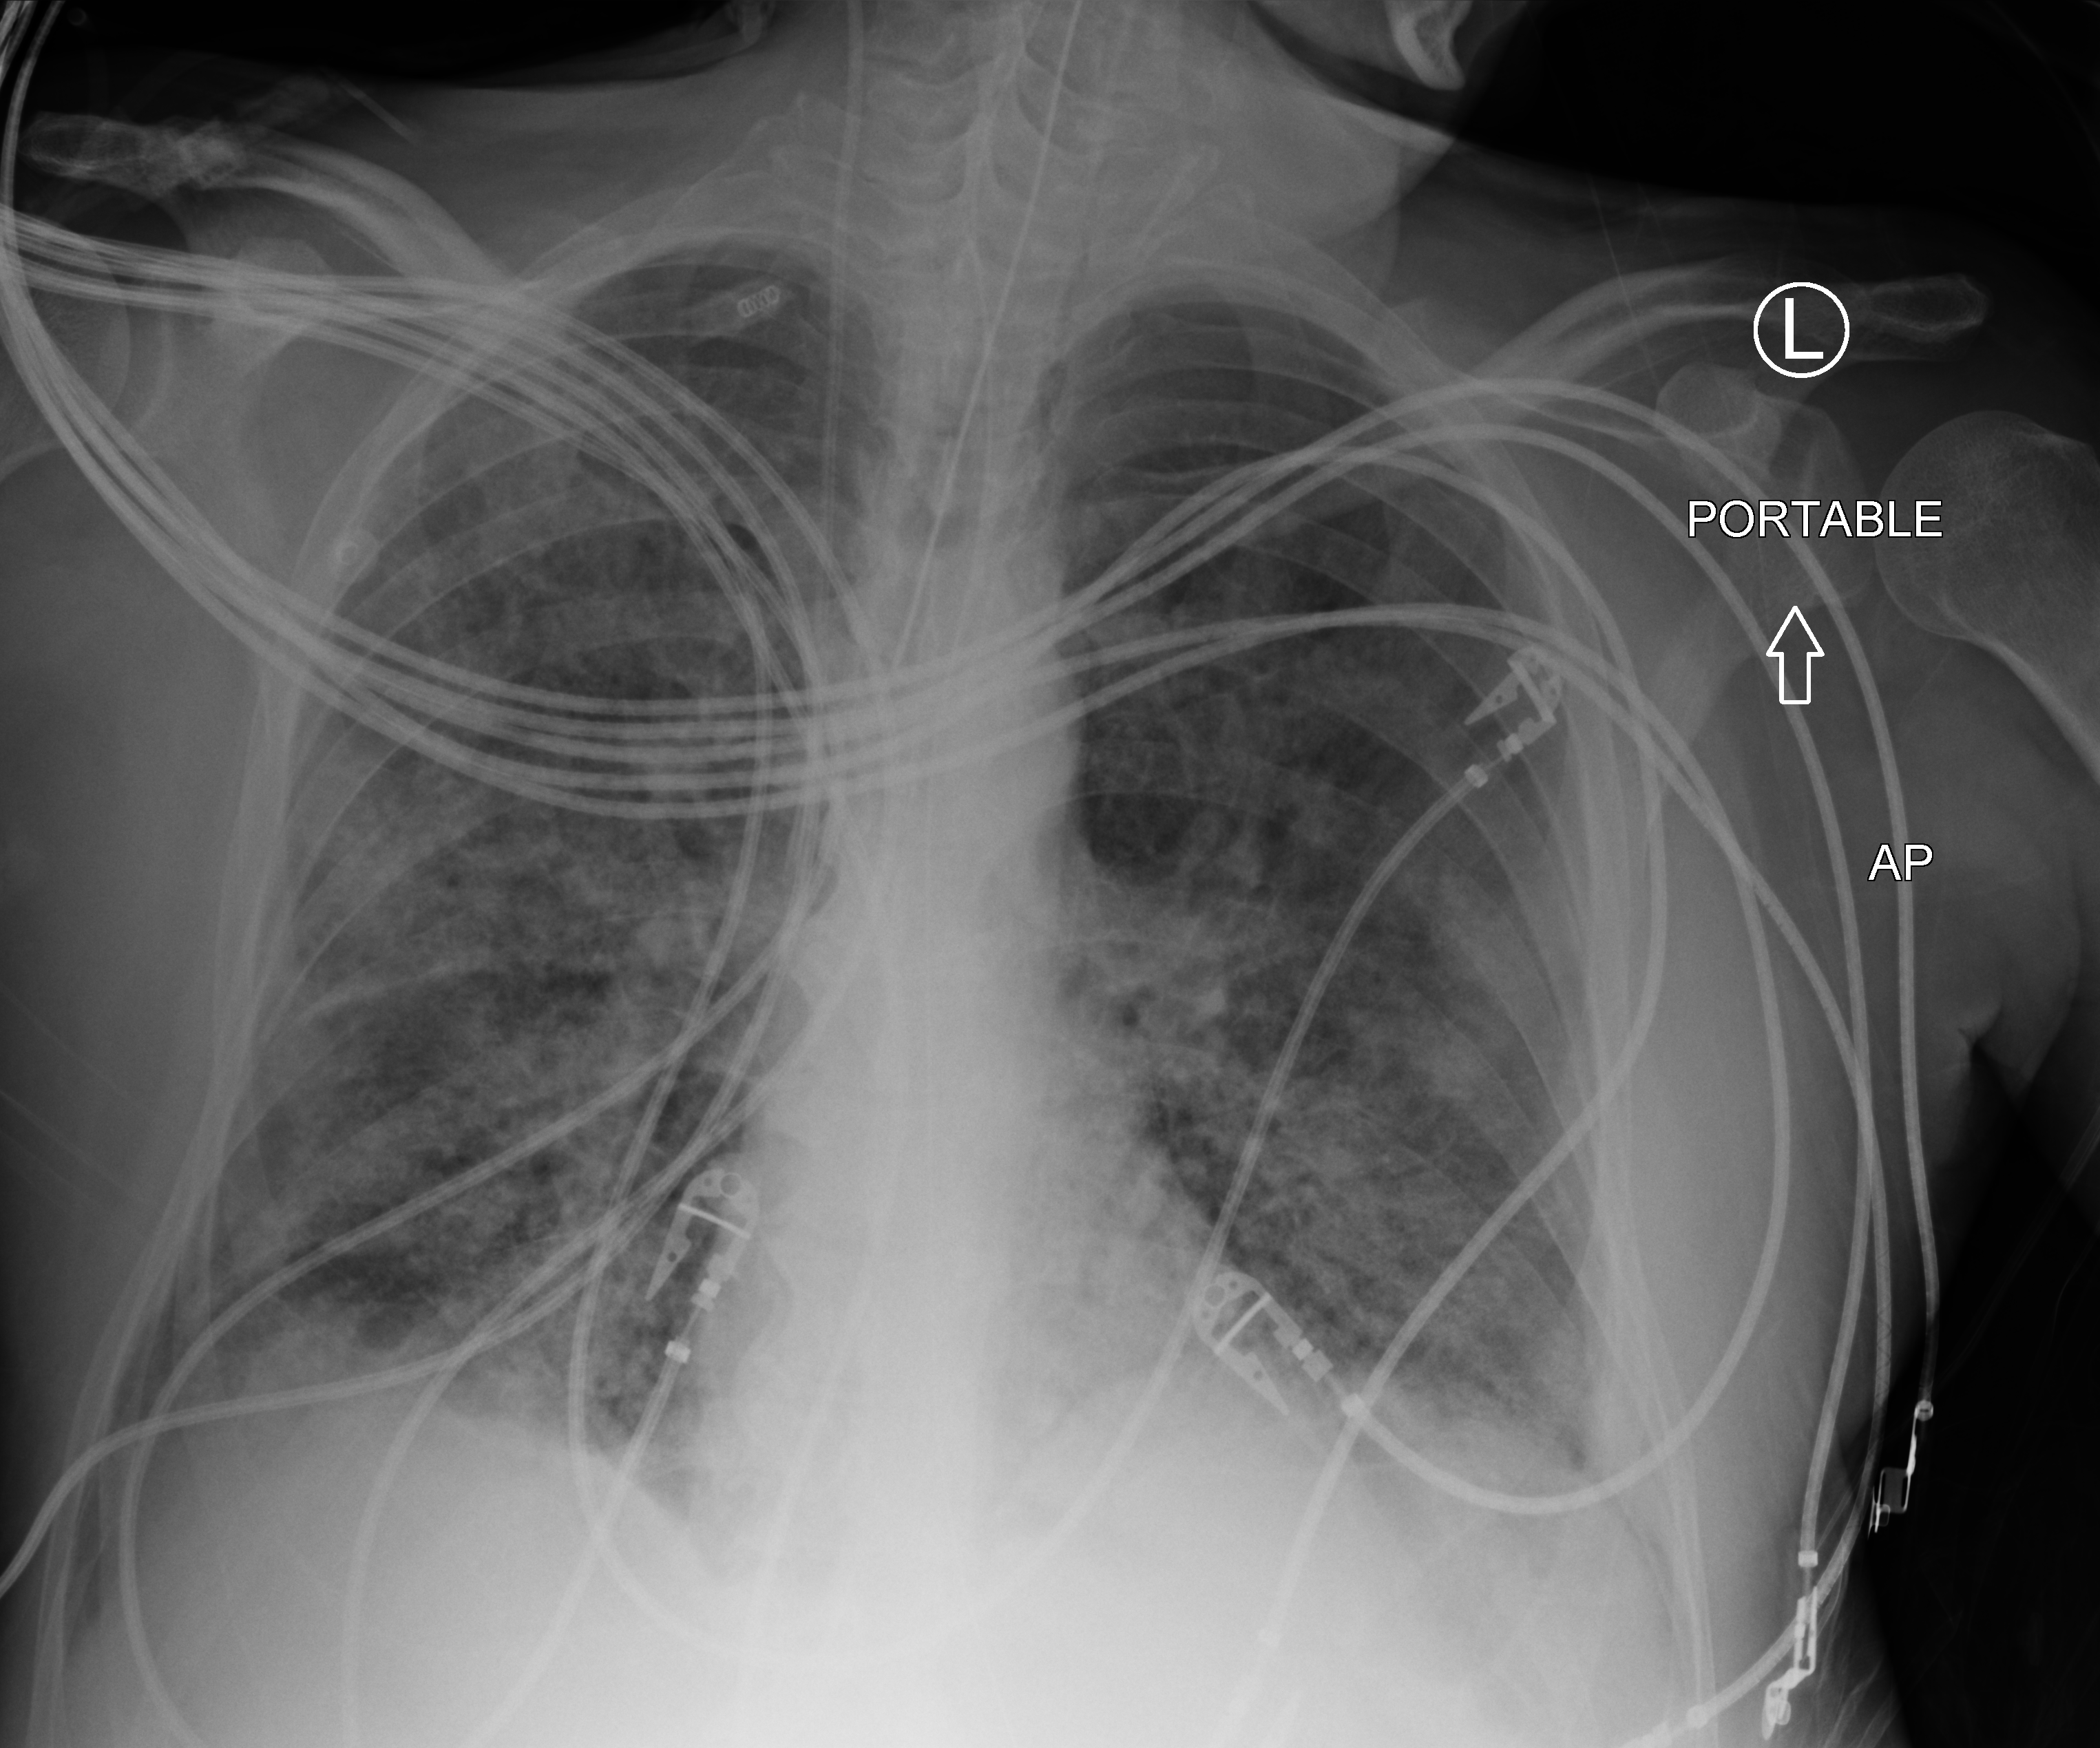
Bedside chest radiograph (computed radiography), anteroposterior (AP) projection. Male patient hospitalised with COVID-19, age 60–74 years.
From the hospital-stay record, not from the radiograph (when in the stay this image was taken is not recorded): admitted to intensive care during this hospital stay: yes; other chronic lung disease (admission record): no; mechanically ventilated during this hospital stay: yes.